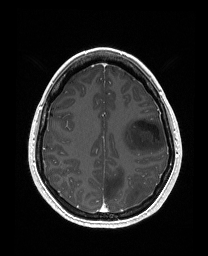
Brain MRI from a brain-tumour surgery series, one axial slice. Slice 114 of 176 in the series (ordered by position). T1-weighted post-contrast. 1 mm slice thickness. 208 × 256 image matrix, field of view 203 × 250 mm. From the clinical record (not read from this slice): histopathology: Astrocytoma; WHO grade: 3; IDH mutation: yes.
Outlined on this slice (outlined manually by an expert reader):
- tumour: bounding box <121,118,166,154> (left, top, right, bottom; pixels)